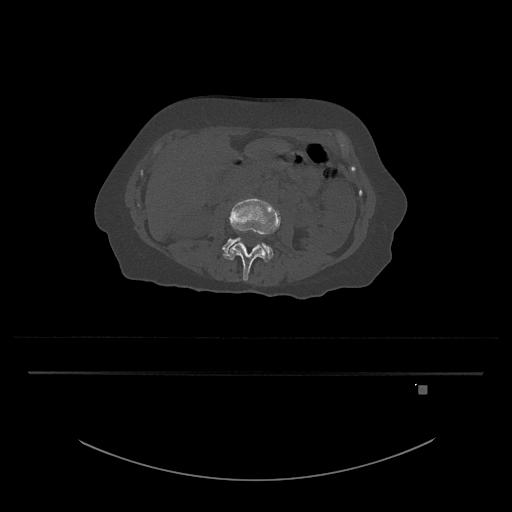
CT including the spine, one axial slice. Slice 407 of 797 in the series (ordered by position). 120 kVp. Bone window (W 1800 / L 400 HU). 0.5 mm slice thickness. 512 × 512 image matrix, field of view 500 × 500 mm. Patient: female, 57 years. From the clinical record (not read from this slice): primary cancer: cervical.
Annotated regions visible in this slice (semi-automatic segmentation, software-assisted and operator-edited):
- L3 vertebra: bounding box [x1, y1, x2, y2] px = [223, 198, 281, 281]
- L4 vertebra: [222, 237, 273, 262]